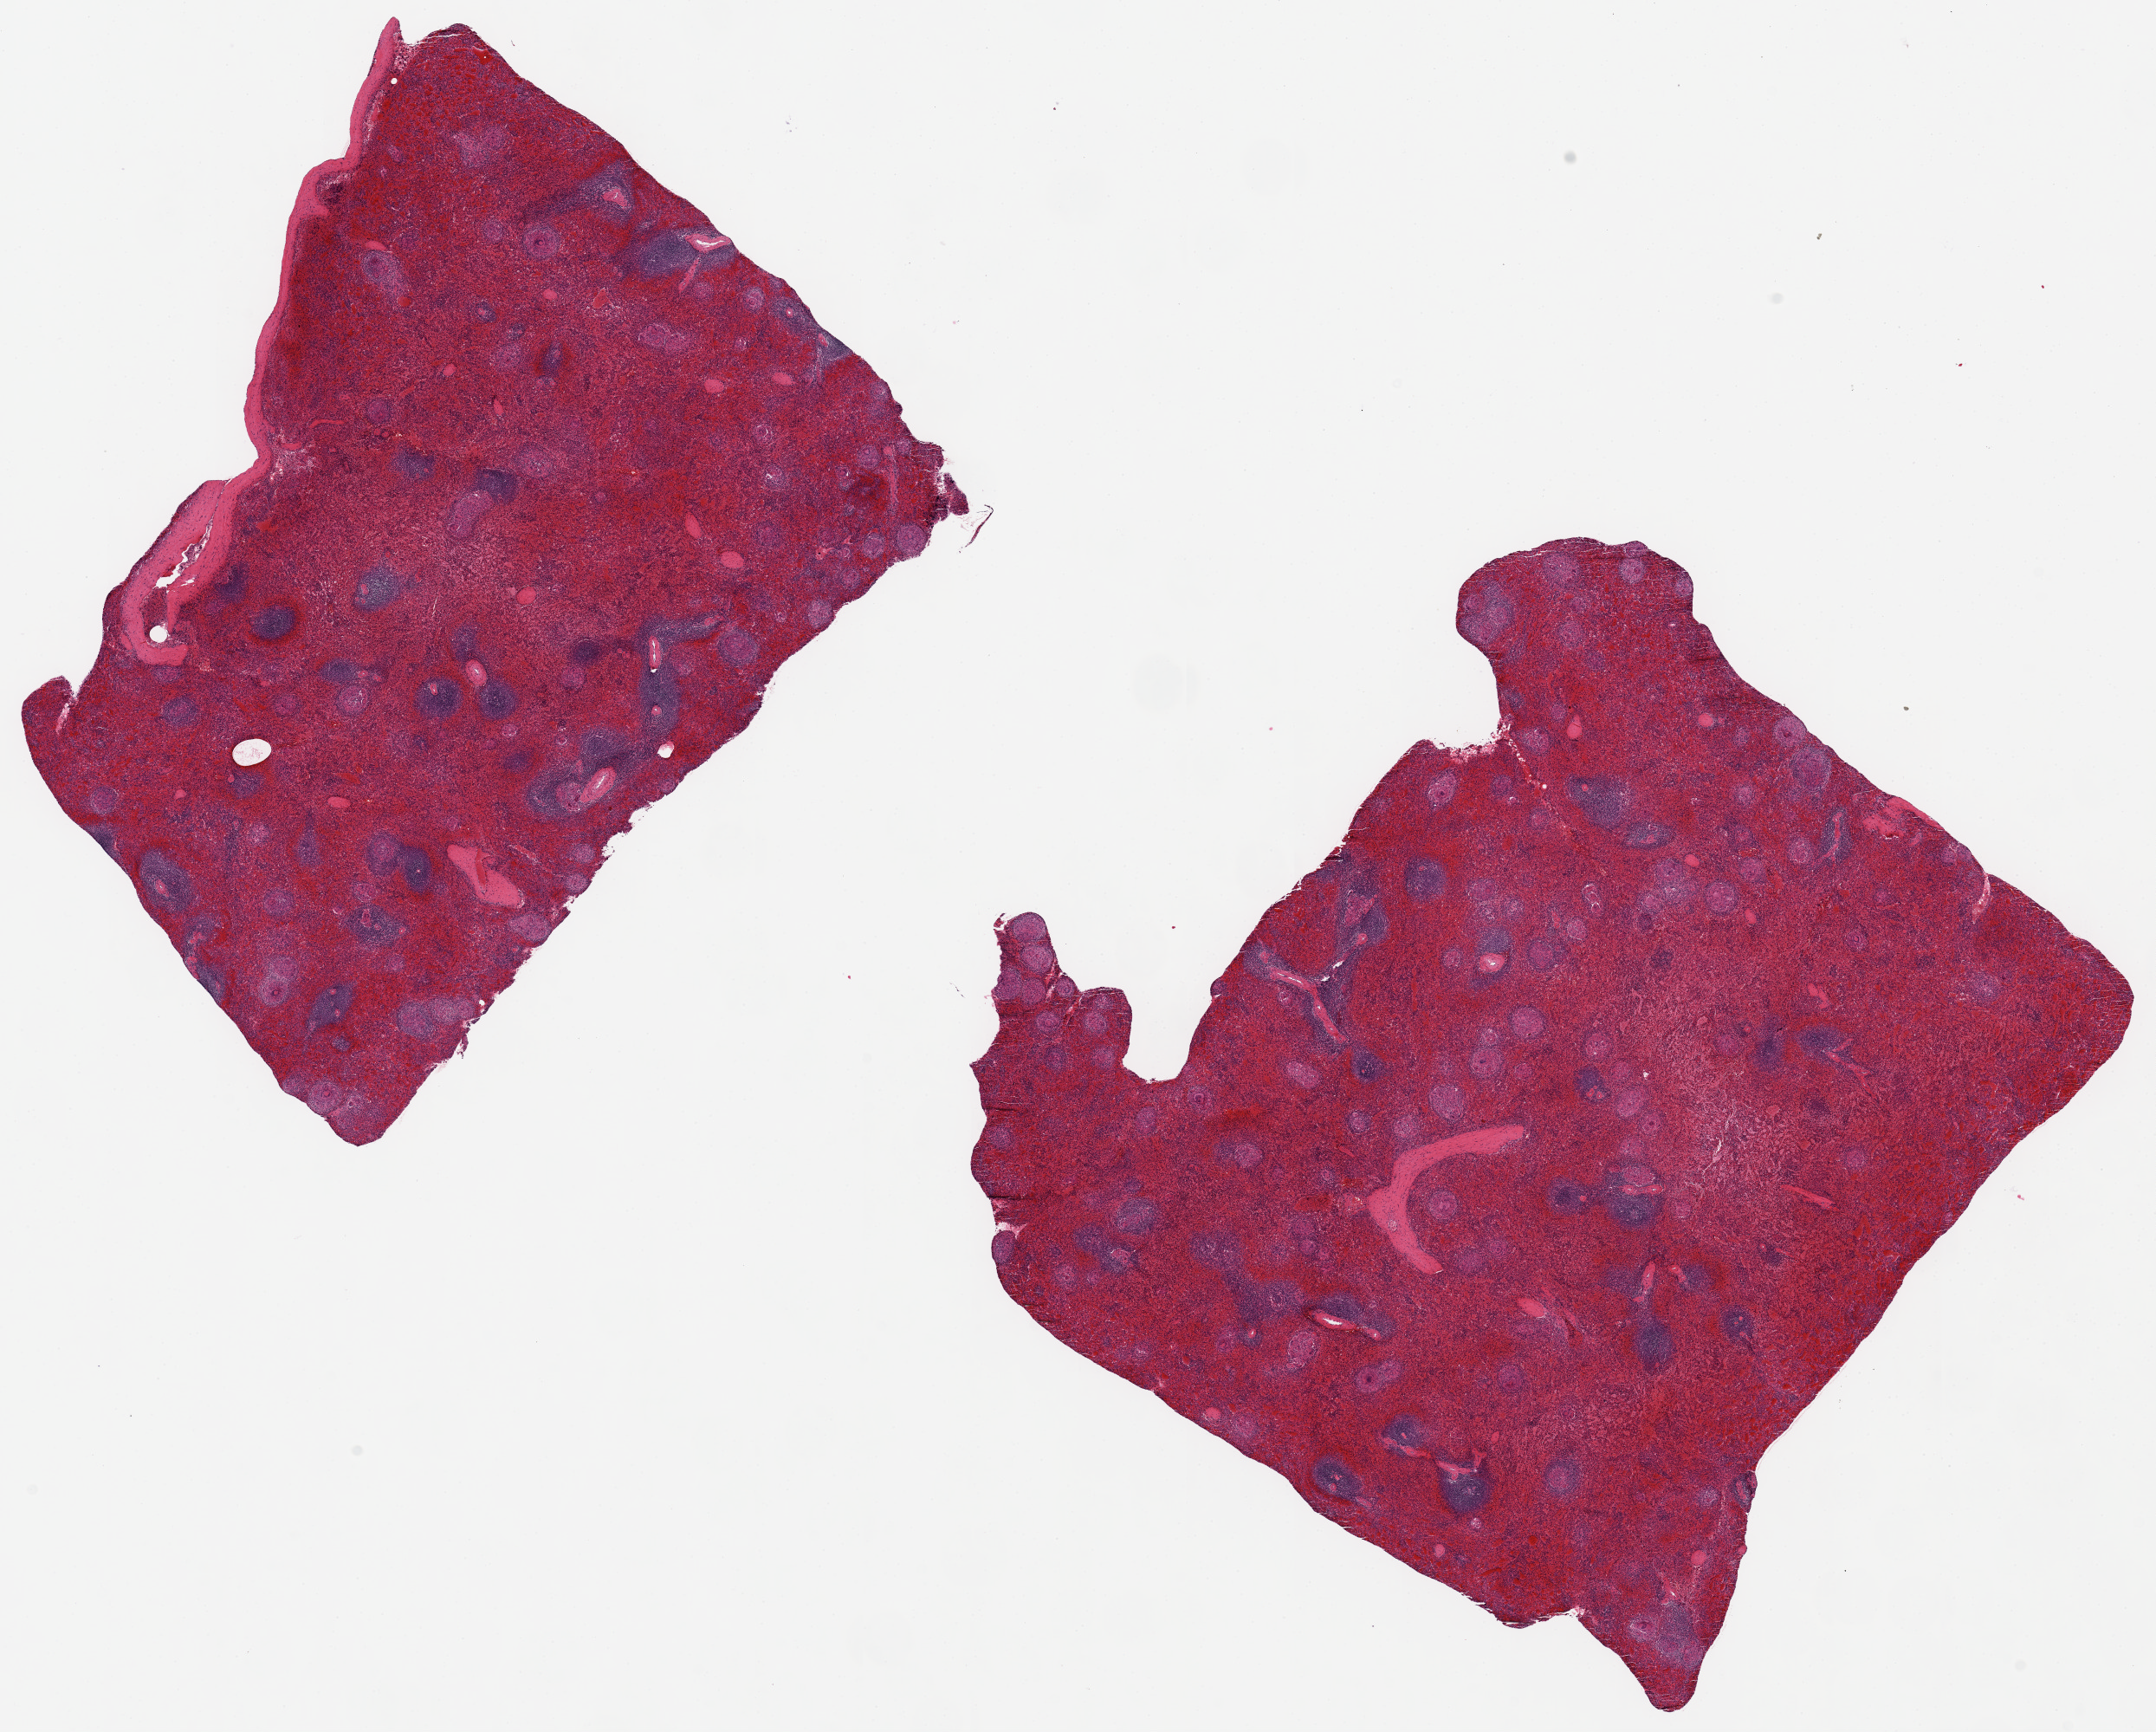
H&E whole-slide image, whole scanned area (about 19.7 x 15.8 mm) shown as a low-resolution overview. PAXgene-fixed paraffin-embedded (PFPE) section. Target tissue: spleen. Tissue donor sample.
* reviewer comment on this tissue sample: 2 pieces, 8.5x7 & 9x9mm; numerous giant cell granulomas, some with asteroid bodies c/w sarcoidosis